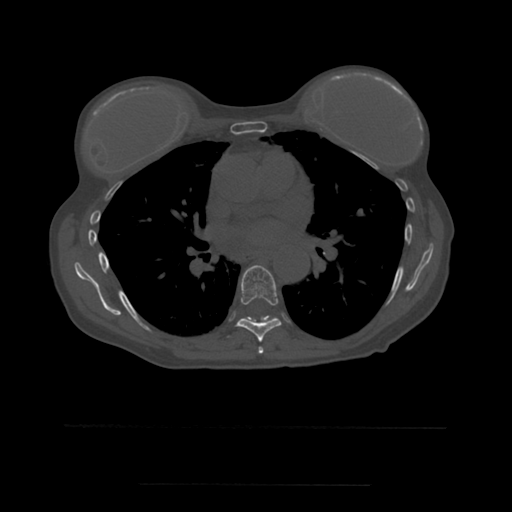
CT including the spine, one axial slice. Slice 356 of 544 in the series (ordered by position). Bone window (W 1800 / L 400 HU). 1.25 mm slice thickness. 512 × 512 image matrix, field of view 350 × 350 mm. Patient age 58 years. From the clinical record (not read from this slice): primary cancer: lung.
Outlined on this slice (semi-automatic segmentation, software-assisted and operator-edited):
- T6 vertebra: bounding box (x1, y1, x2, y2) in pixels: (258, 347, 264, 354)
- T7 vertebra: (236, 265, 282, 342)
- T8 vertebra: (261, 317, 273, 322)